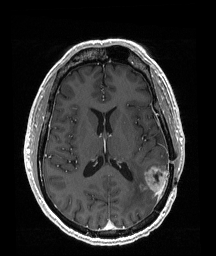
Brain MRI from a brain-tumour surgery series, one axial slice. Position 85 of 192 along the scan axis. T1-weighted post-contrast. 216 × 256 image matrix, field of view 211 × 250 mm. Case-level facts recorded for this patient, not image findings: histopathology: Glioblastoma; WHO grade: 4; IDH mutation: no.
Structures marked on this image (outlined manually by an expert reader):
- tumour: bounding box <144,166,170,197> (left, top, right, bottom; pixels)